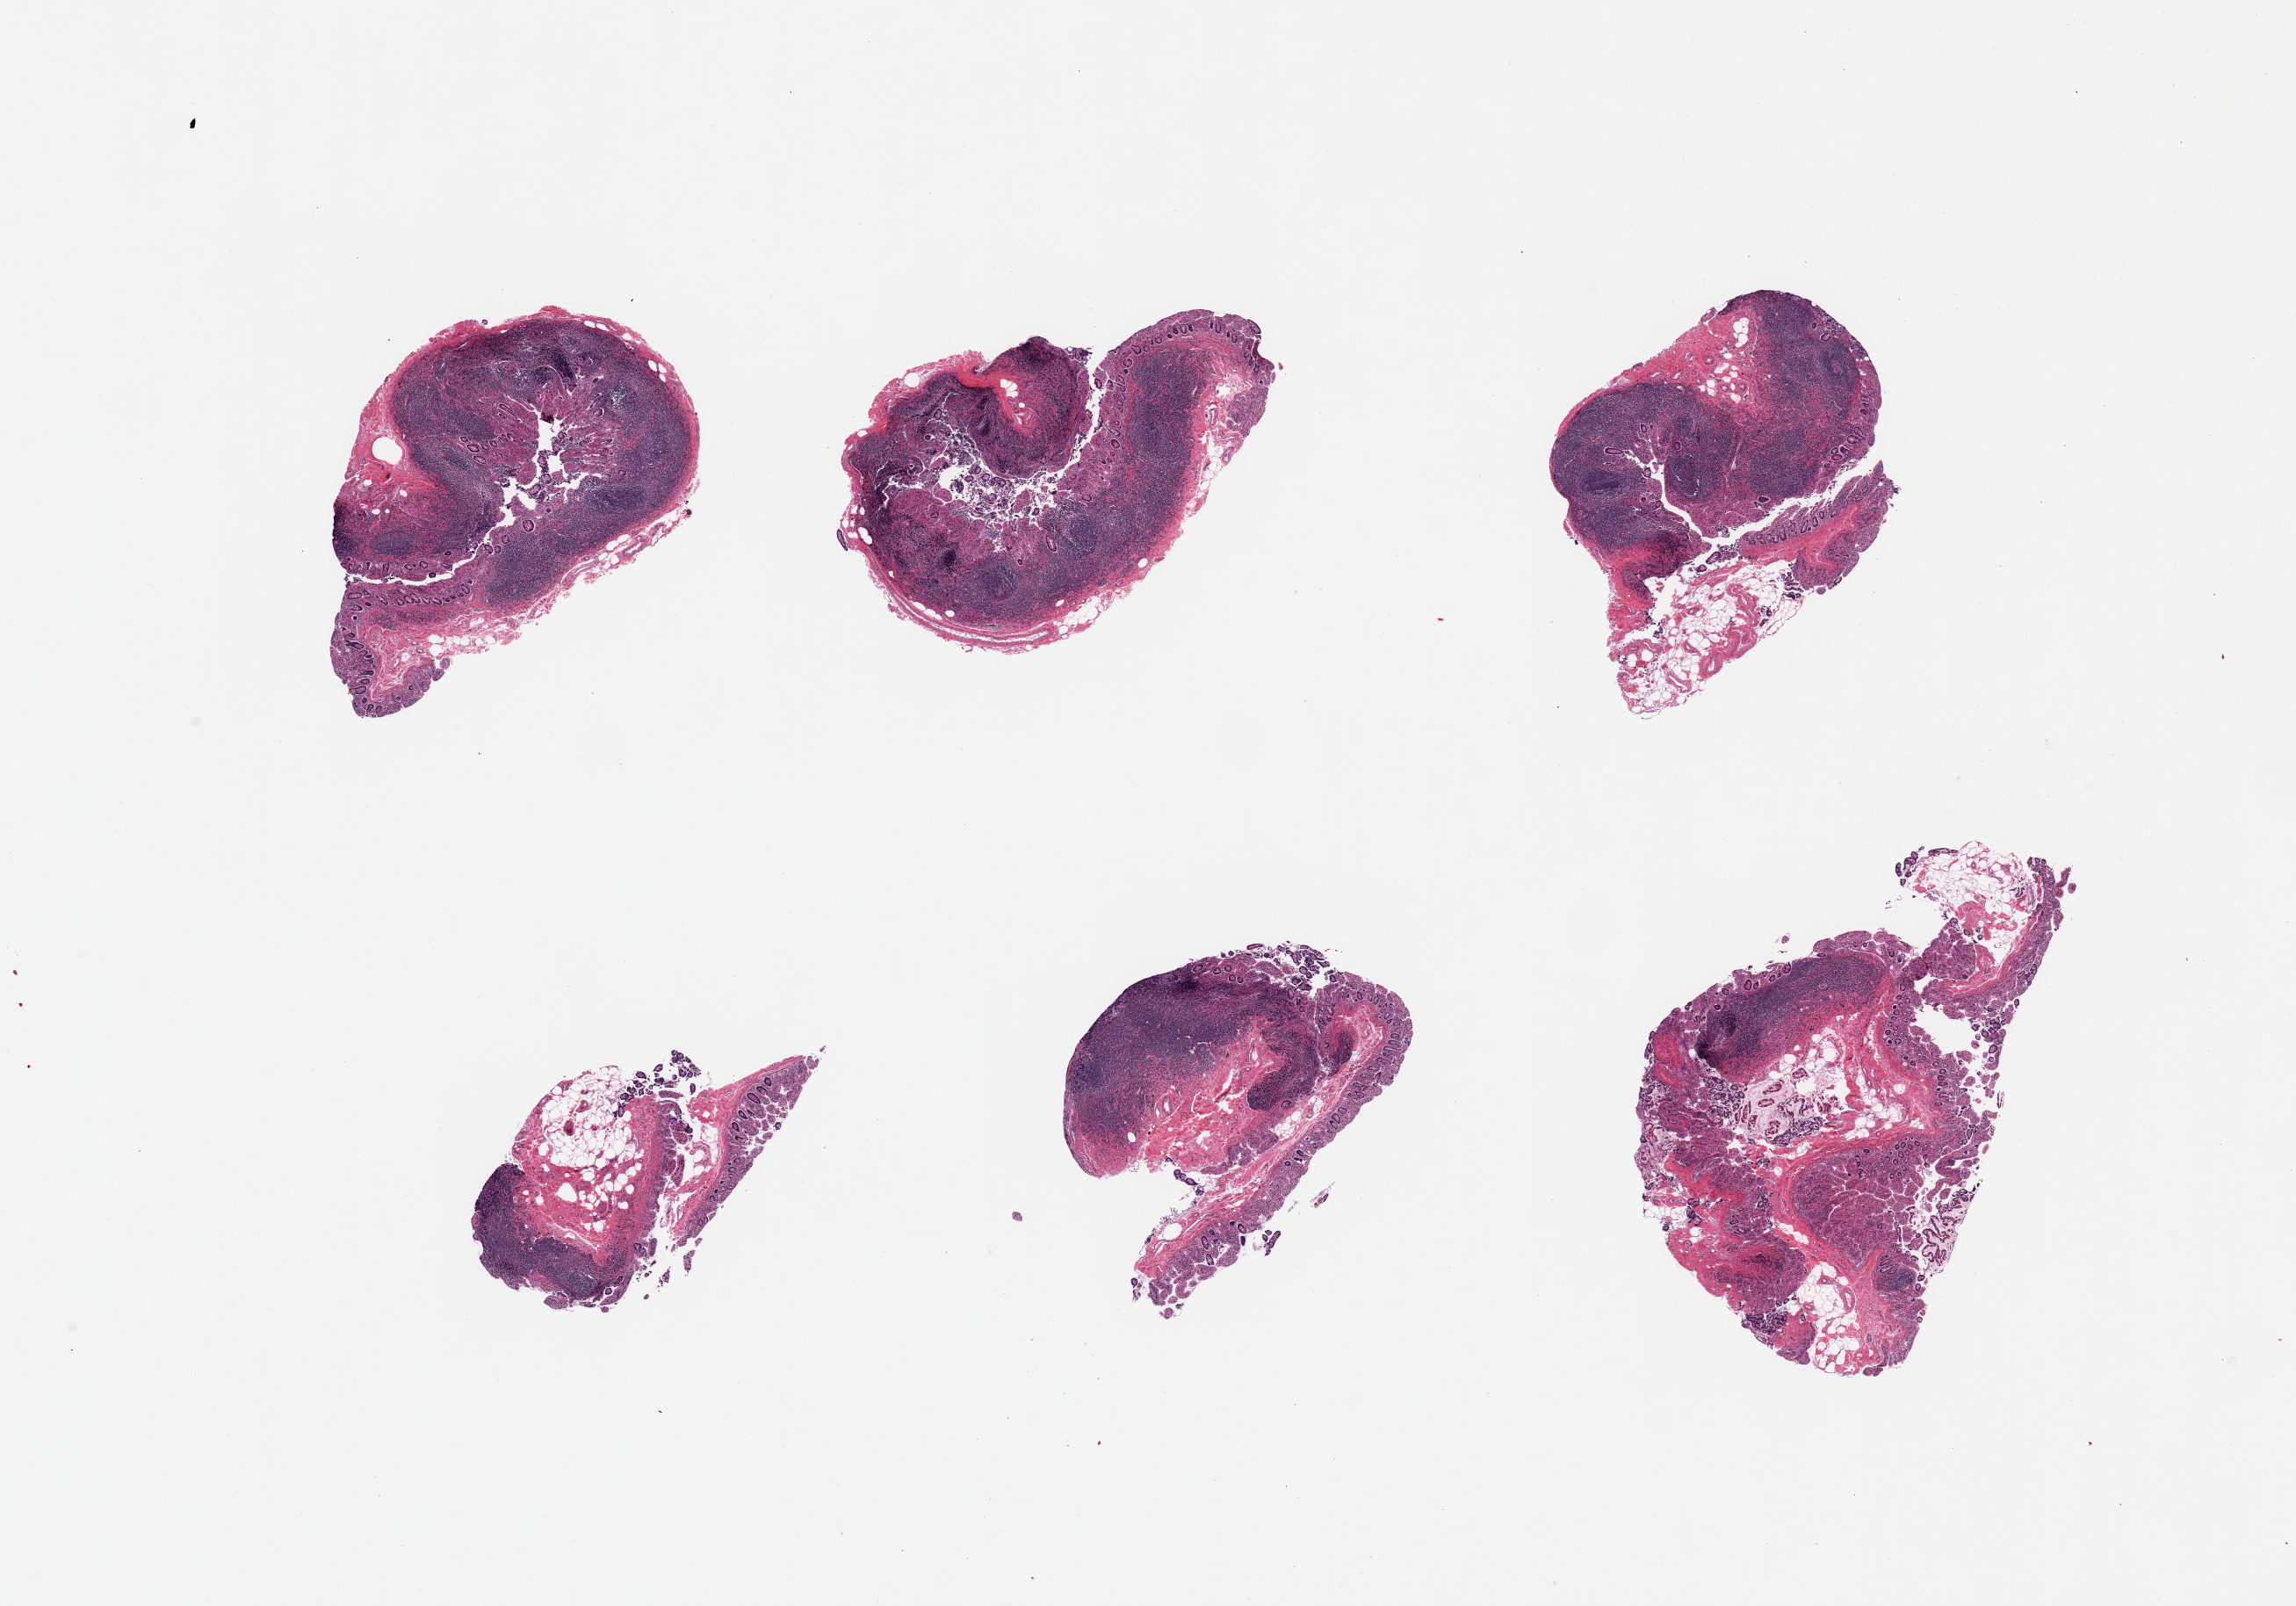
Hematoxylin and eosin (H&E) whole-slide image, brightfield — low-resolution overview of the scanned area, about 20.7 x 14.5 mm; PAXgene-fixed paraffin-embedded (PFPE) section; section of ileum (target tissue); donor tissue sample. Donor: male.
Reviewer comment on this tissue sample: 6 pieces, target lymphoid aggregates ~40% of tissue.